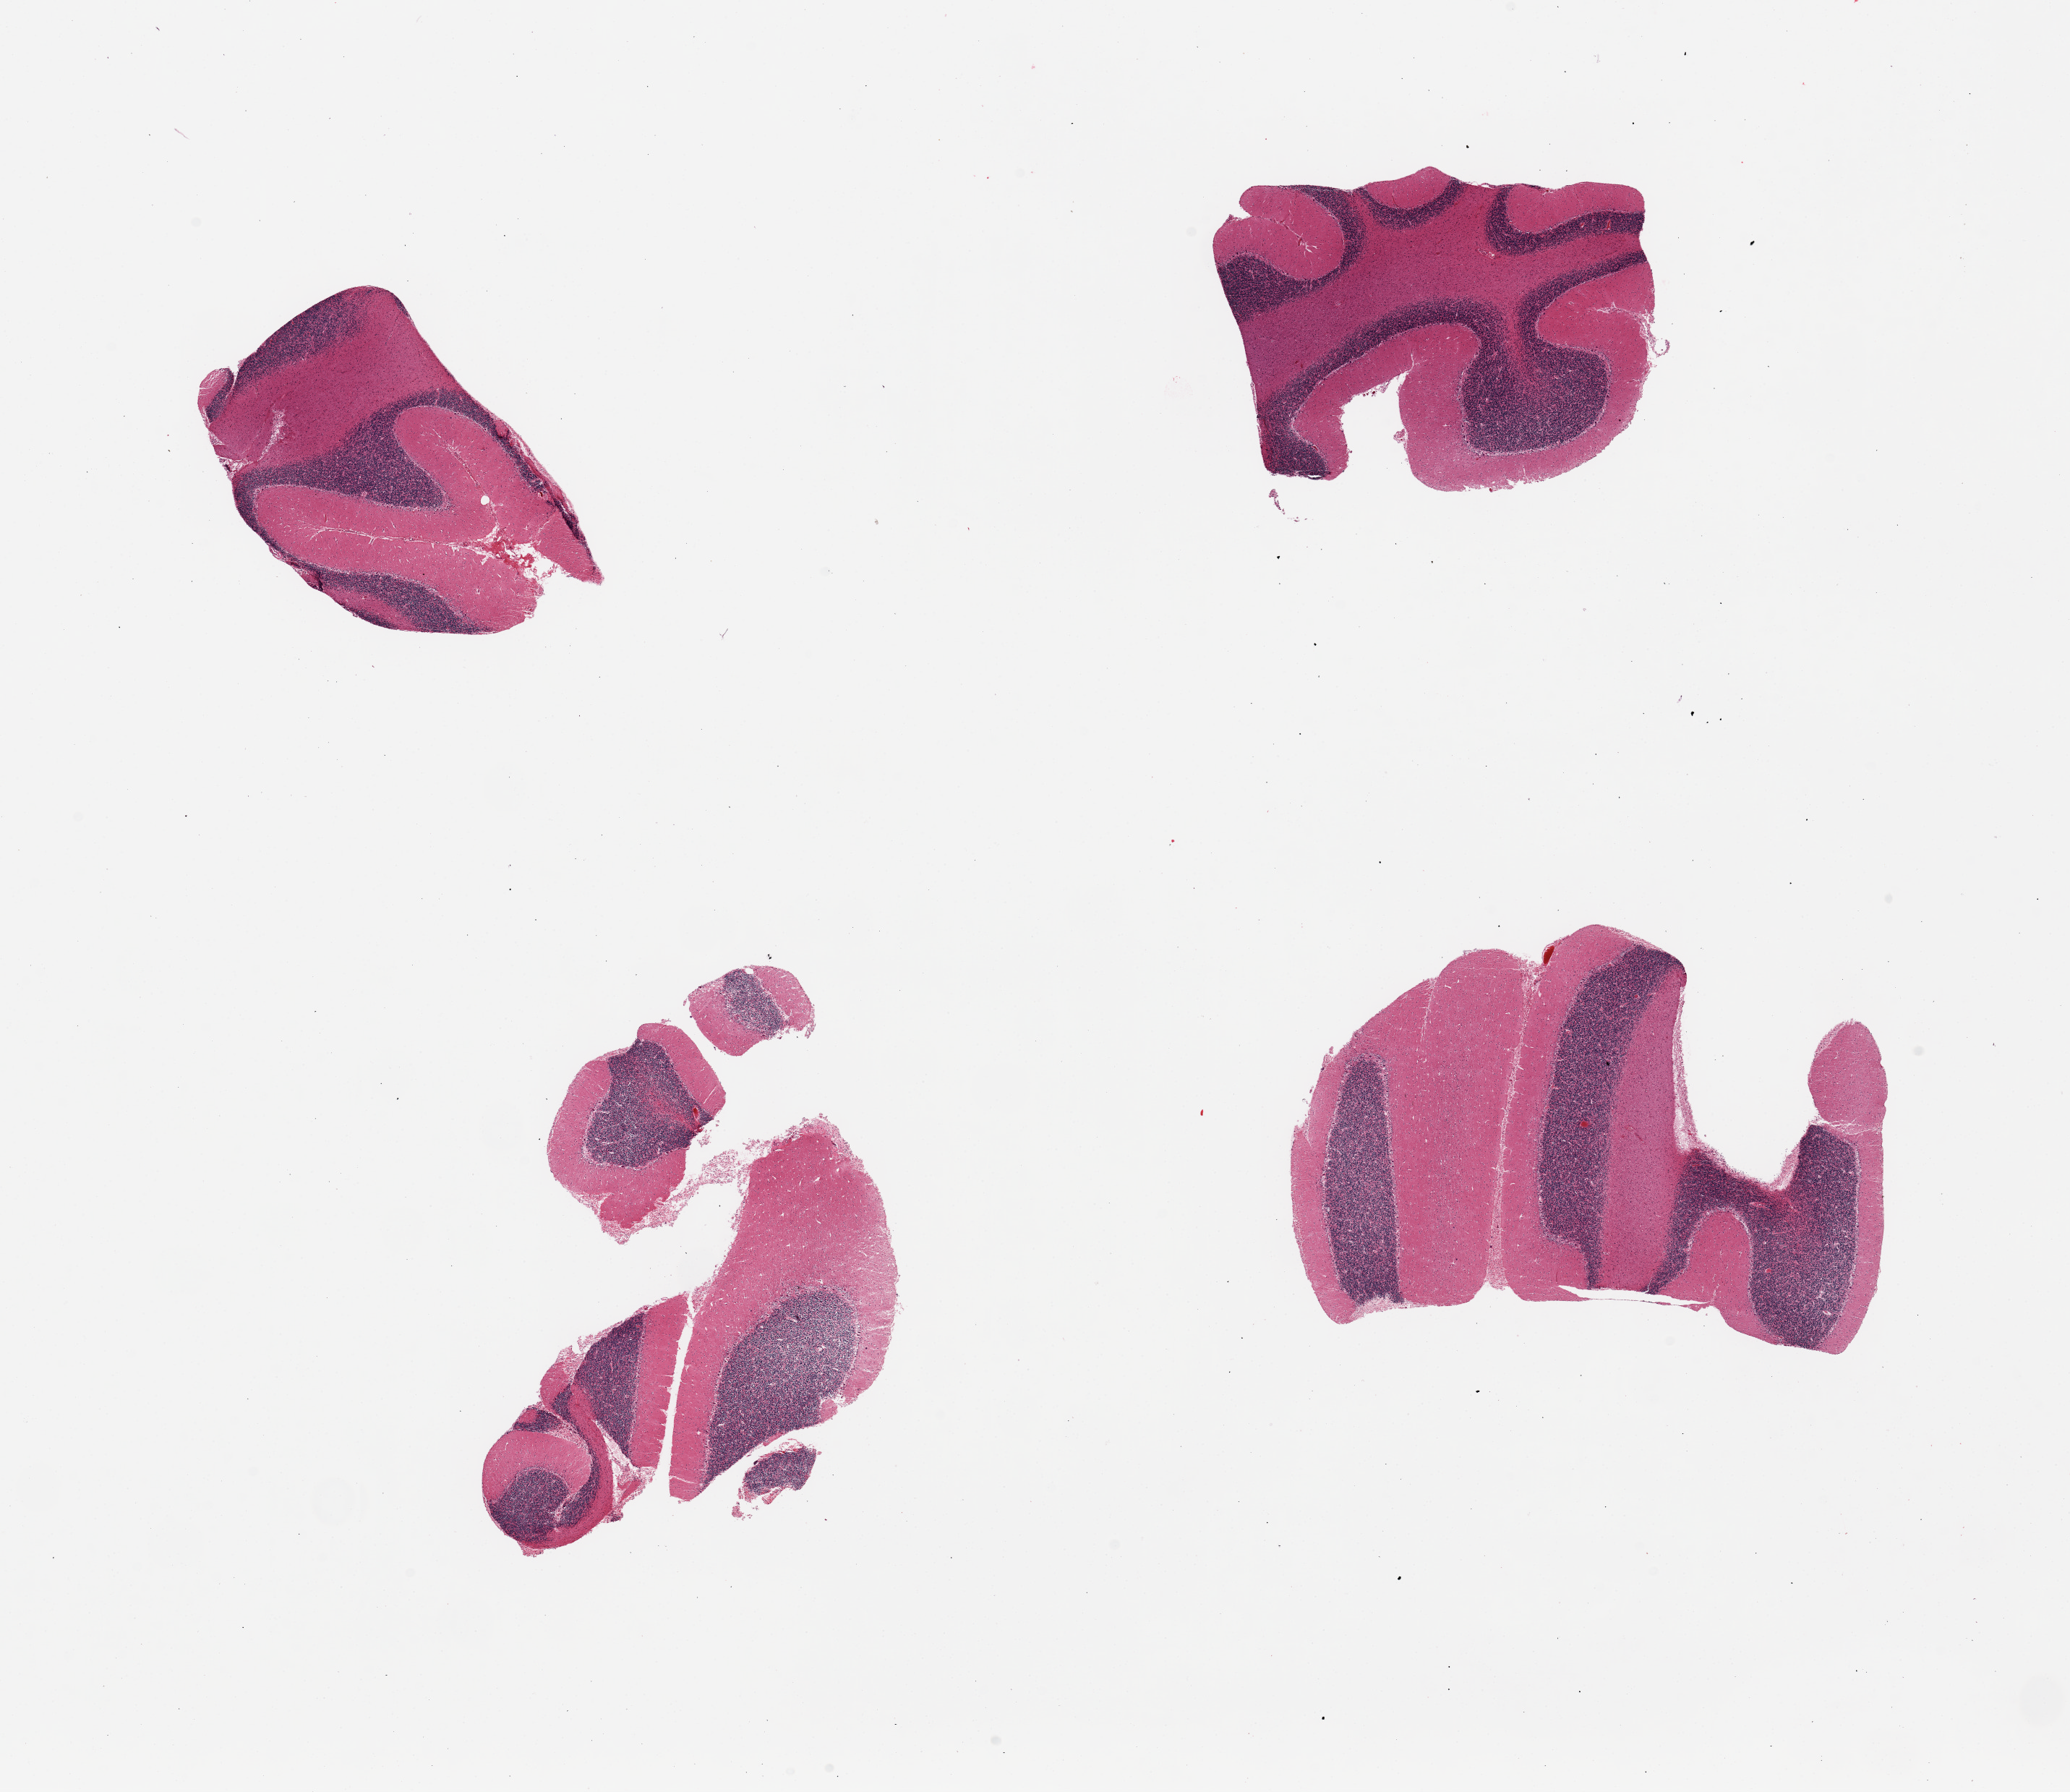
Whole-slide image, hematoxylin and eosin (H&E) stain, shown as a low-resolution overview of the whole scanned area (about 22.6 x 19.6 mm, from a 20x scan), PAXgene-fixed paraffin-embedded (PFPE) section, section of cerebellum (target tissue), tissue donor sample. Donor: male.
Review note (as recorded): 3 pieces.